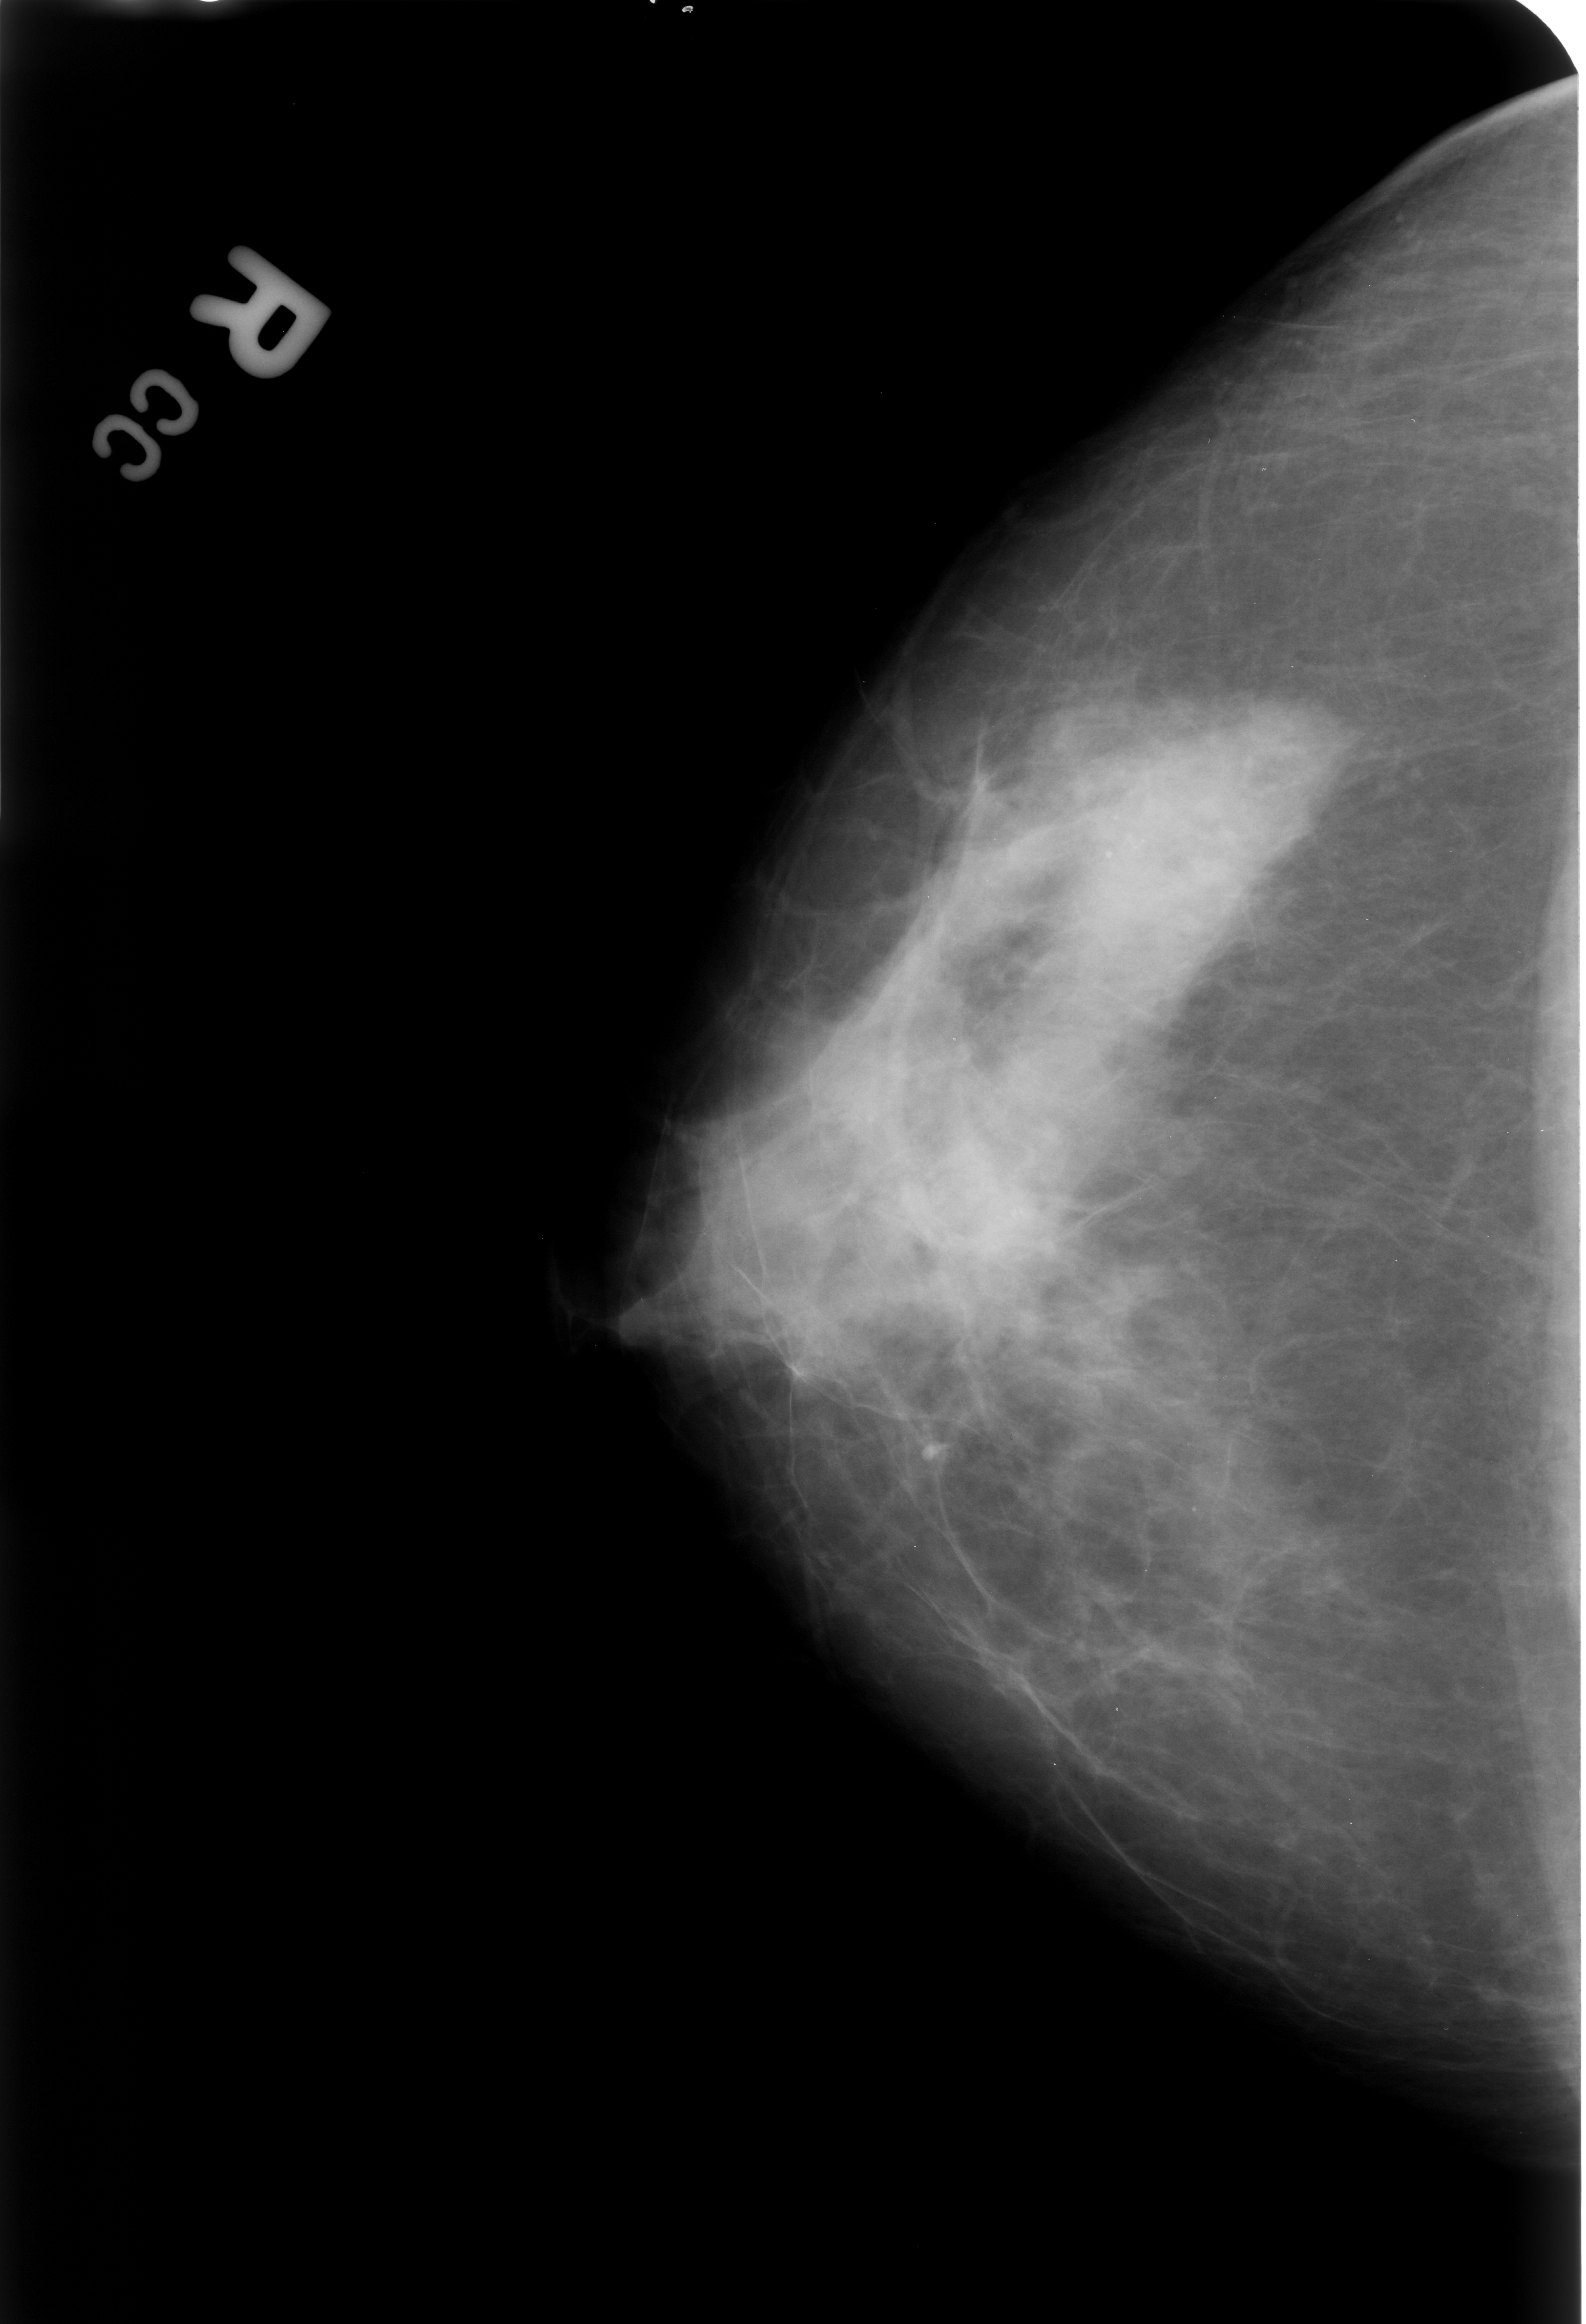
Scanned film-screen mammogram; right breast; CC view.
Radiologist-marked abnormalities on this image: Finding 1 of 2: calcifications, morphology punctate / round and regular, distribution regional; BI-RADS assessment category 2; benign without callback (not worked up further). Finding 2 of 2: calcifications, morphology punctate / round and regular, distribution regional; BI-RADS assessment category 2; subtlety rating 3 on a 1 (subtle) to 5 (obvious) scale; benign without callback (not worked up further).